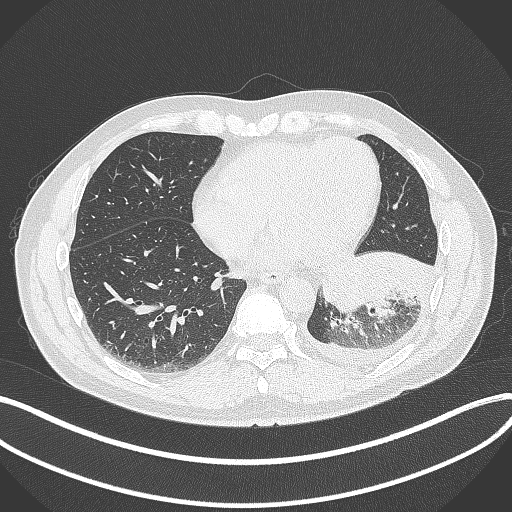
Chest CT, one axial slice. 120 kVp. Lung window (W 1500 / L -600 HU). 1 mm slice thickness. 512 × 512 image matrix. Patient: male, 58 years. Case-level facts recorded for this patient, not image findings: clinical TNM (as recorded): T3 N1 M1b; histopathological grade: G3.
Annotated regions visible in this slice (bounding box drawn by a radiologist):
- lung tumour (recorded histology: small cell carcinoma): box from (x=319, y=242) to (x=438, y=317) px